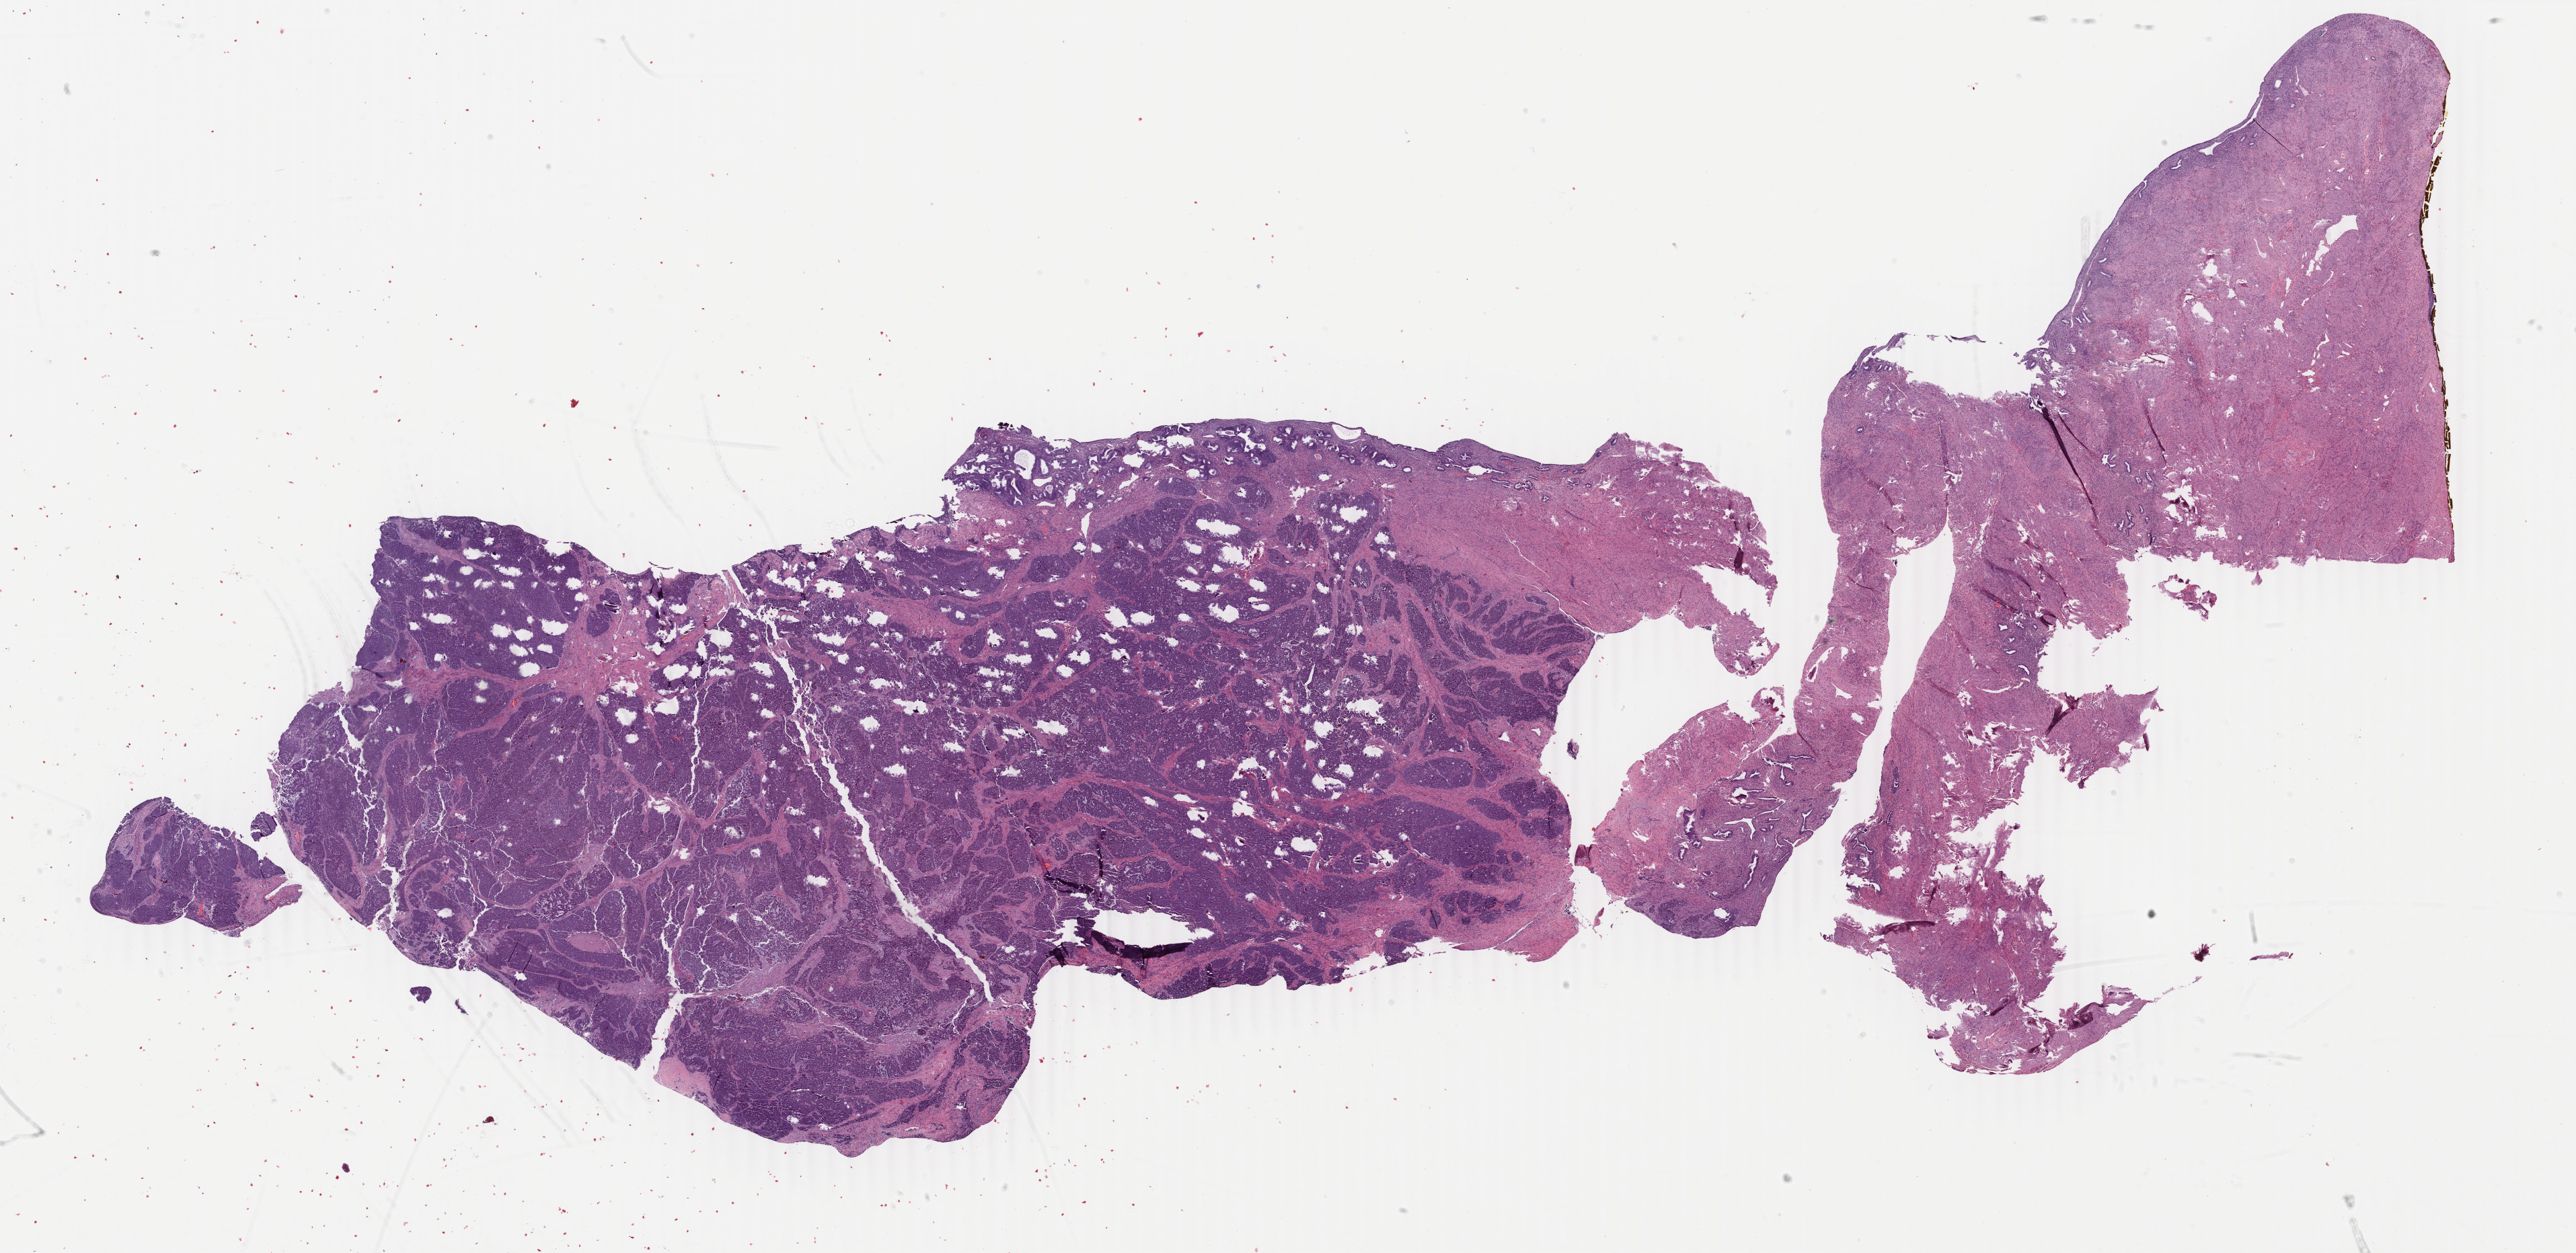
Whole-slide histology image, Hematoxylin and eosin (H&E) stained, low-resolution overview of the scanned area, about 30.5 x 14.8 mm (slide scanned at 40x), FFPE section, primary tumour sample from the uterus. Female, age 64 years at initial diagnosis. Histologic grade: G3 (poorly differentiated).
FIGO stage: IB. Diagnosis: Endometrioid adenocarcinoma, NOS (endometrium).